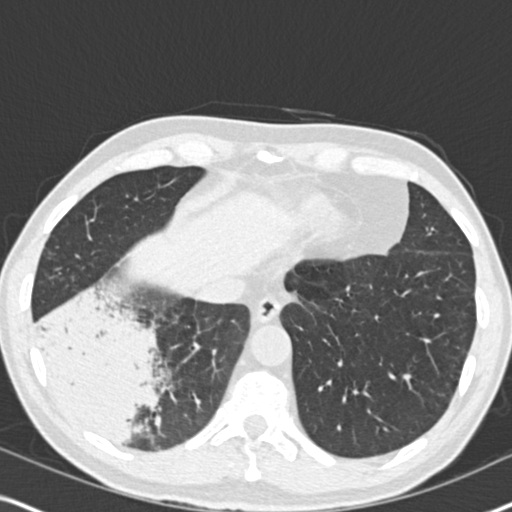
Axial slice from a low-dose chest CT screening exam. Second annual screen. Lung window (W 1500 / L -600 HU). 2 mm slice thickness. 512 × 512 image matrix, field of view 330 × 330 mm. Male, age 61 years at enrolment. Current smoker at enrolment.
Expert-annotated lung lesion, box from (x=29, y=294) to (x=183, y=458) px. Reader record for this screening exam (exam-level; its link to the box is not recorded): non-calcified nodule or mass ≥4 mm, right lower lobe, 90 × 80 mm, soft tissue attenuation, pre-existing on the prior screen: yes; interval growth: yes. Lung cancer was diagnosed 20 days after this screen: bronchiolo-alveolar adenocarcinoma, NOS, right lower lobe, moderately differentiated (G2), stage IIIB (AJCC 6th edition), 90 mm at pathology.